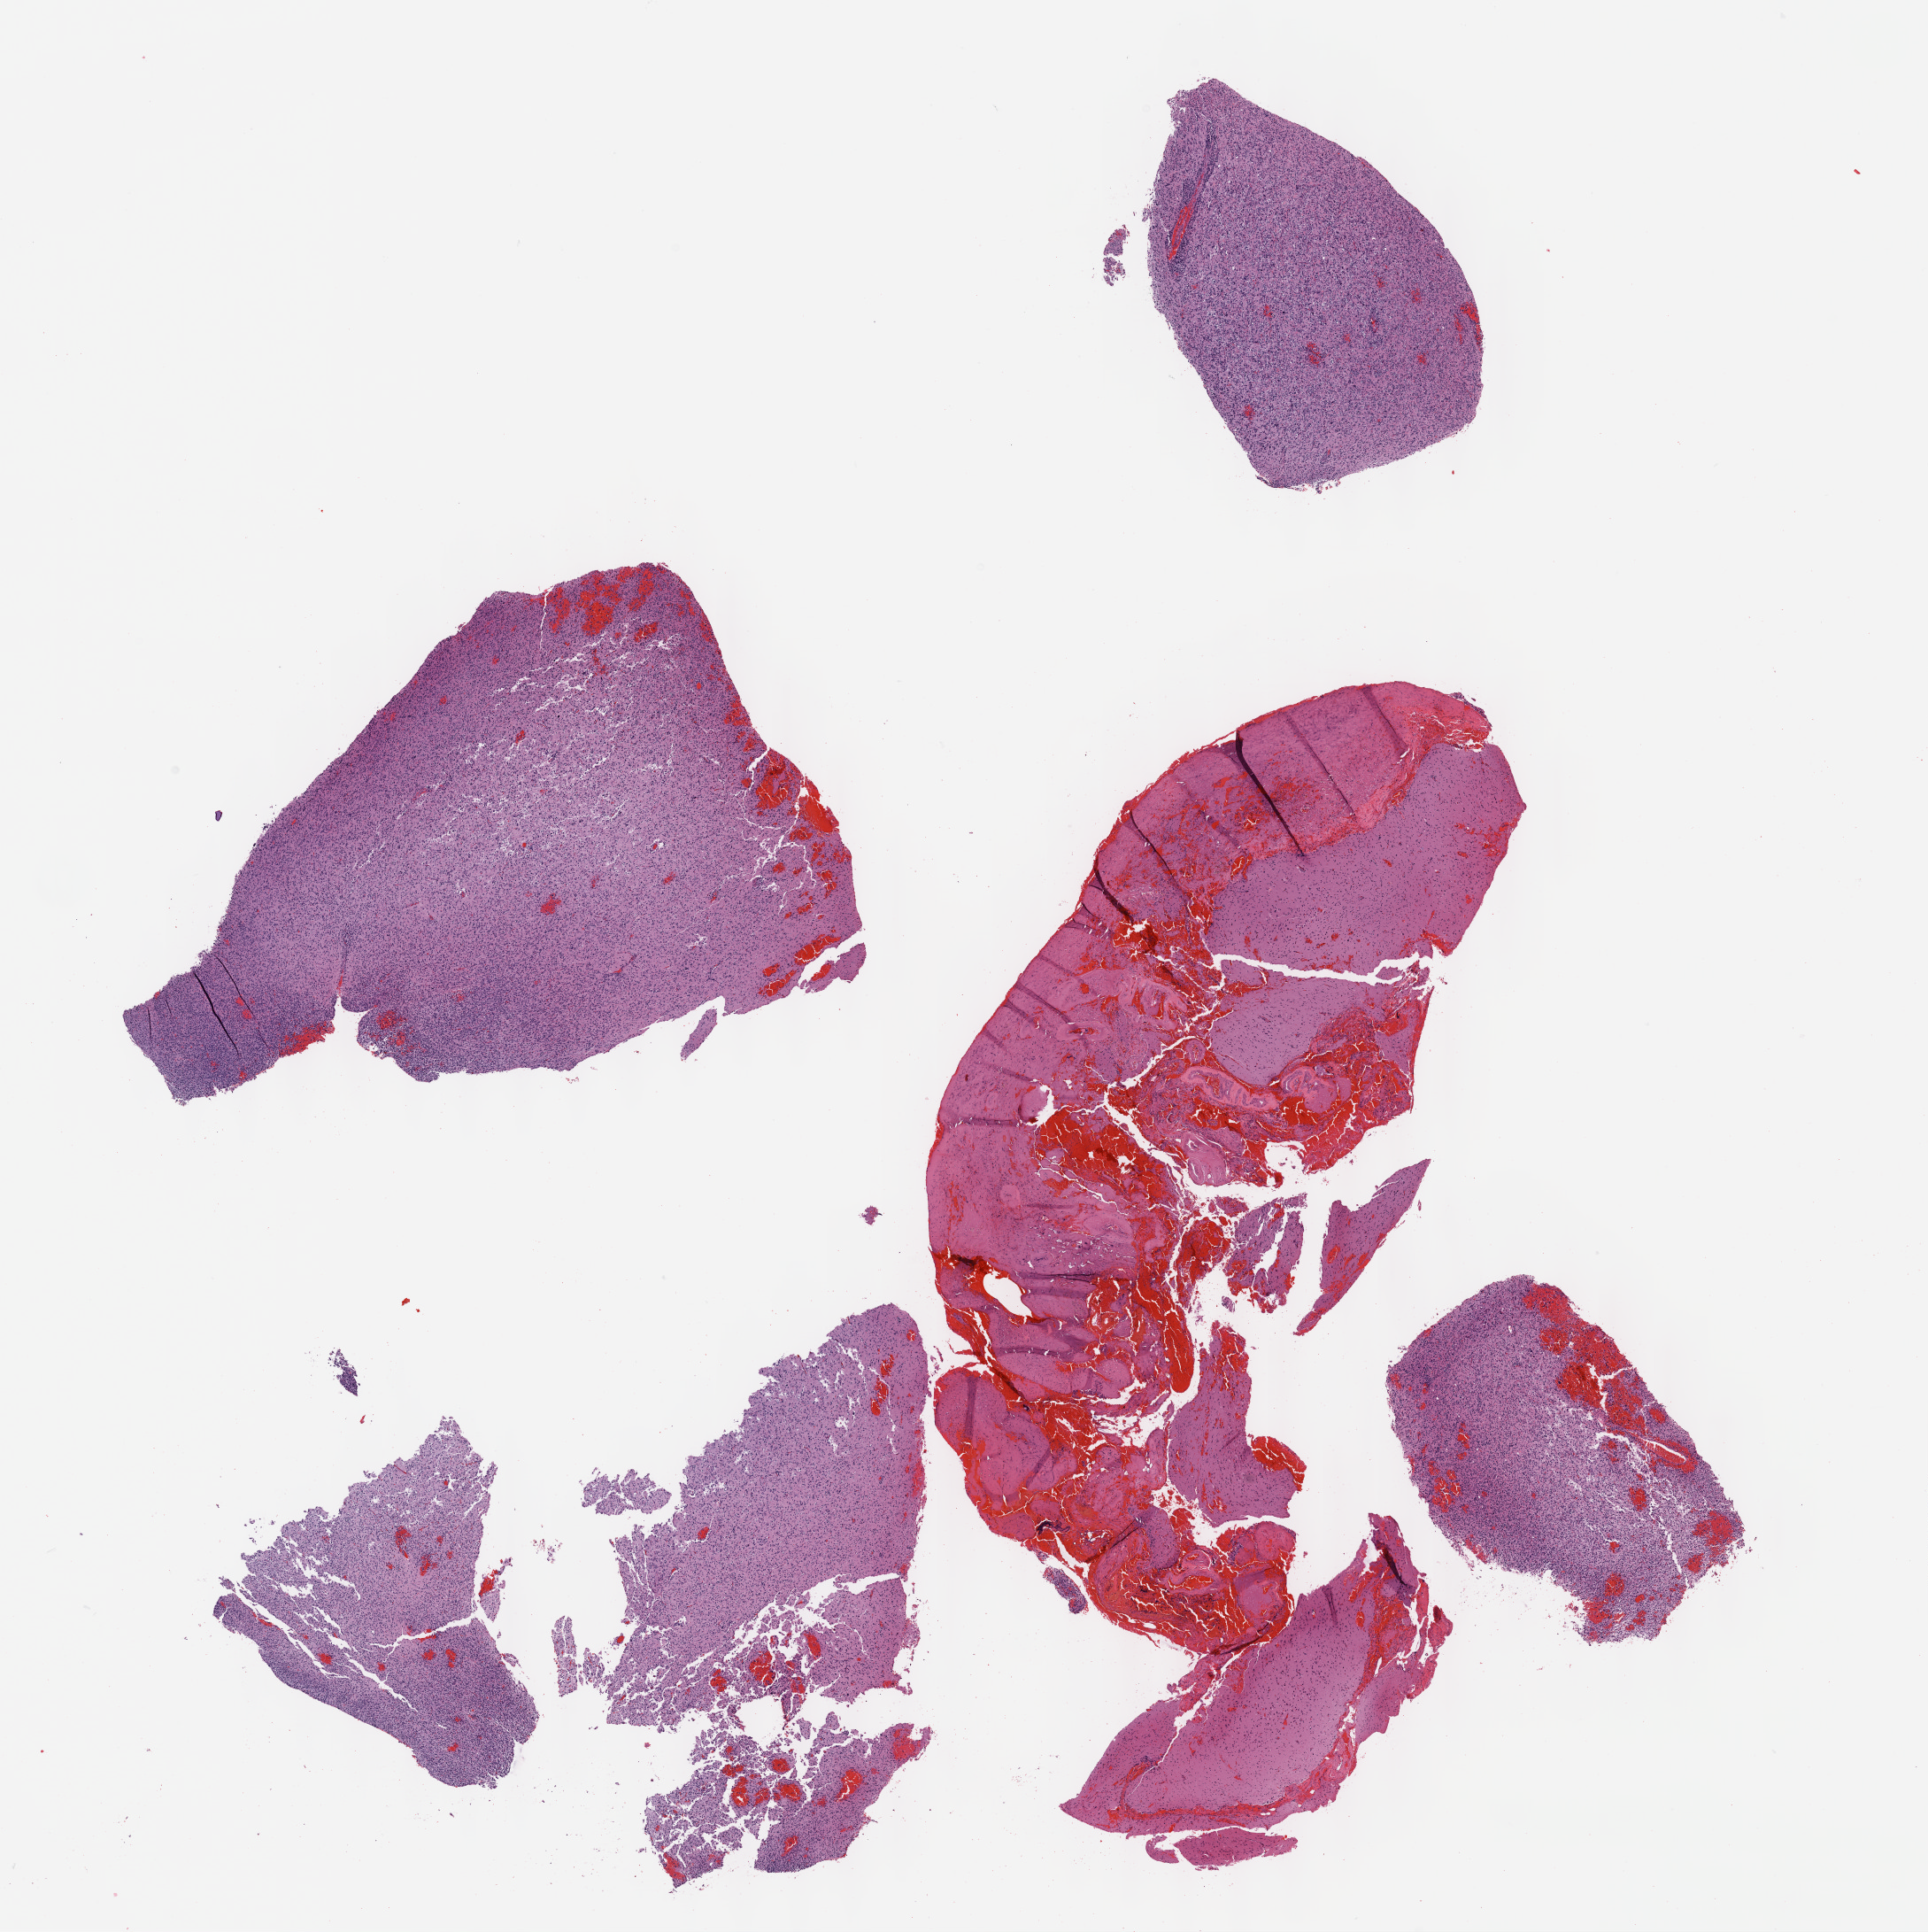
H&E whole-slide image — shown as a low-resolution overview of the whole scanned area (about 17.6 x 17.6 mm, acquisition: 40x scan). Formalin-fixed paraffin-embedded (FFPE) diagnostic section. Brain, primary tumour sample. Patient: male, age at initial diagnosis 62 years. Histologic grade: G3 (poorly differentiated).
* laterality: left
* diagnosis: Astrocytoma, anaplastic (cerebrum)